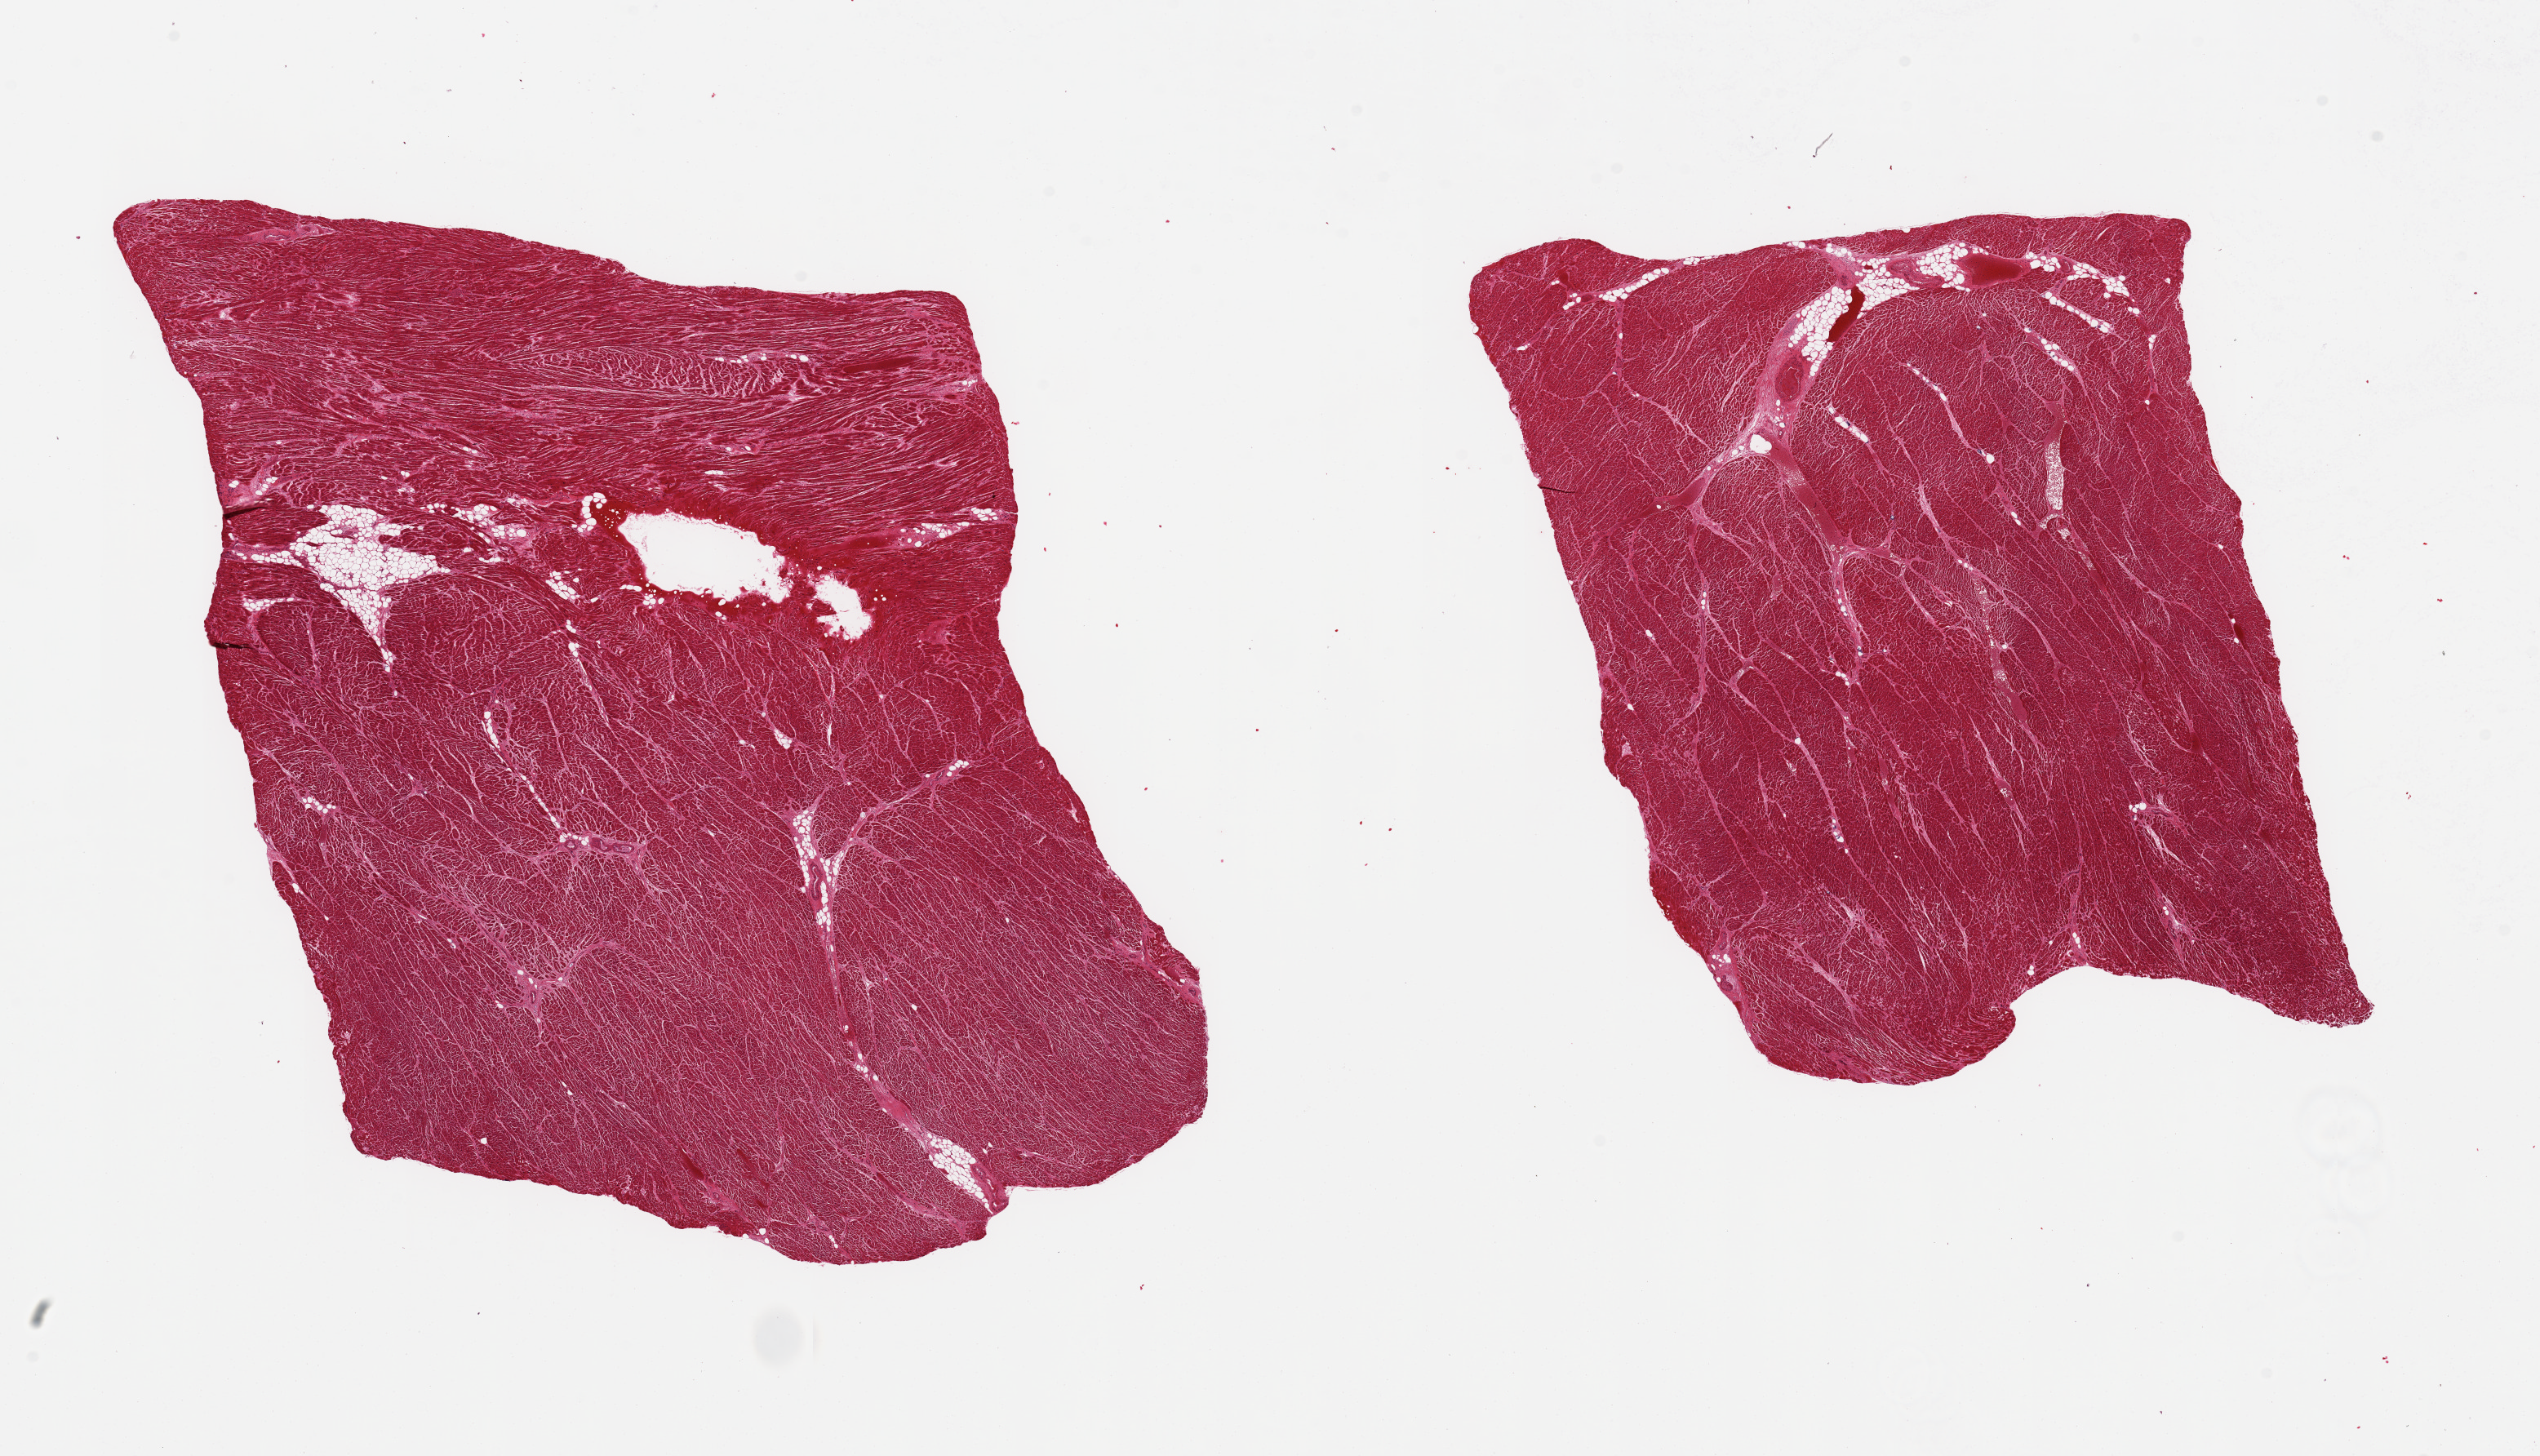
Digitized haematoxylin and eosin-stained section, low-resolution overview of the scanned area, about 24.6 x 14.1 mm; PAXgene-fixed paraffin-embedded (PFPE) section; target tissue: heart; tissue donor sample. Male donor.
Pathologist's review note for this sample: 2 pieces, mild-moderate interstitial fibrosis, chronic ischemic changes.